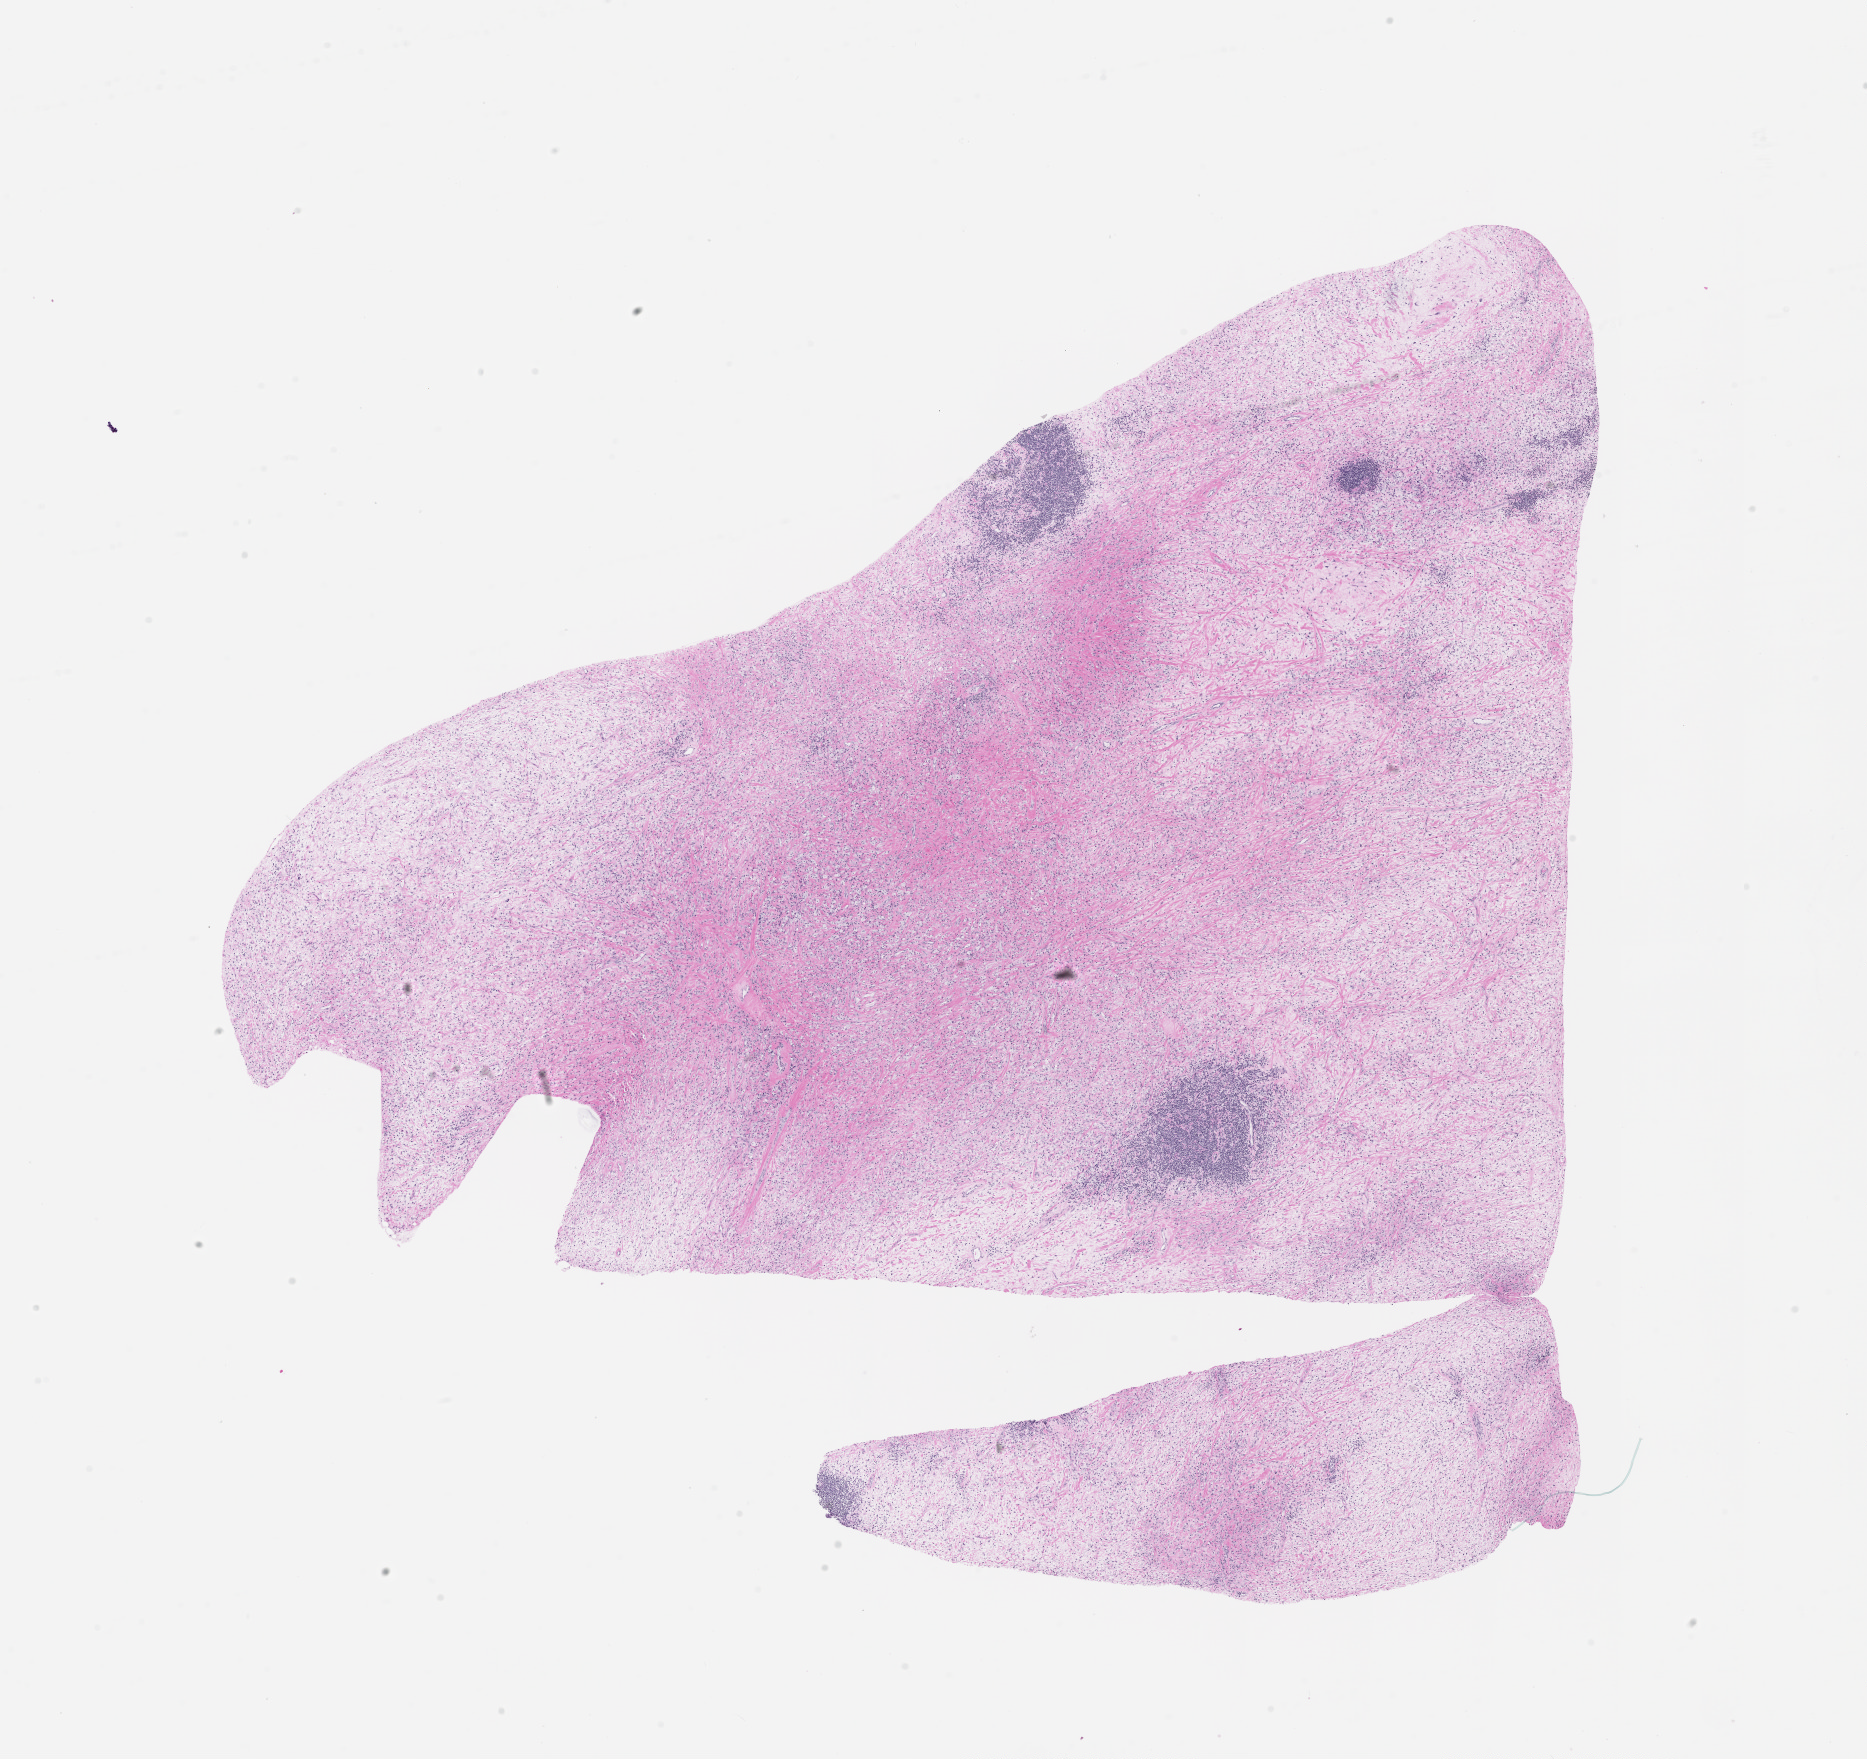
Digitized H&E tissue section (whole slide) — low-resolution overview of the scanned area, about 15.0 x 14.2 mm.
Patient diagnosis (cohort enrolment): sarcoma (site not recorded at cohort level).